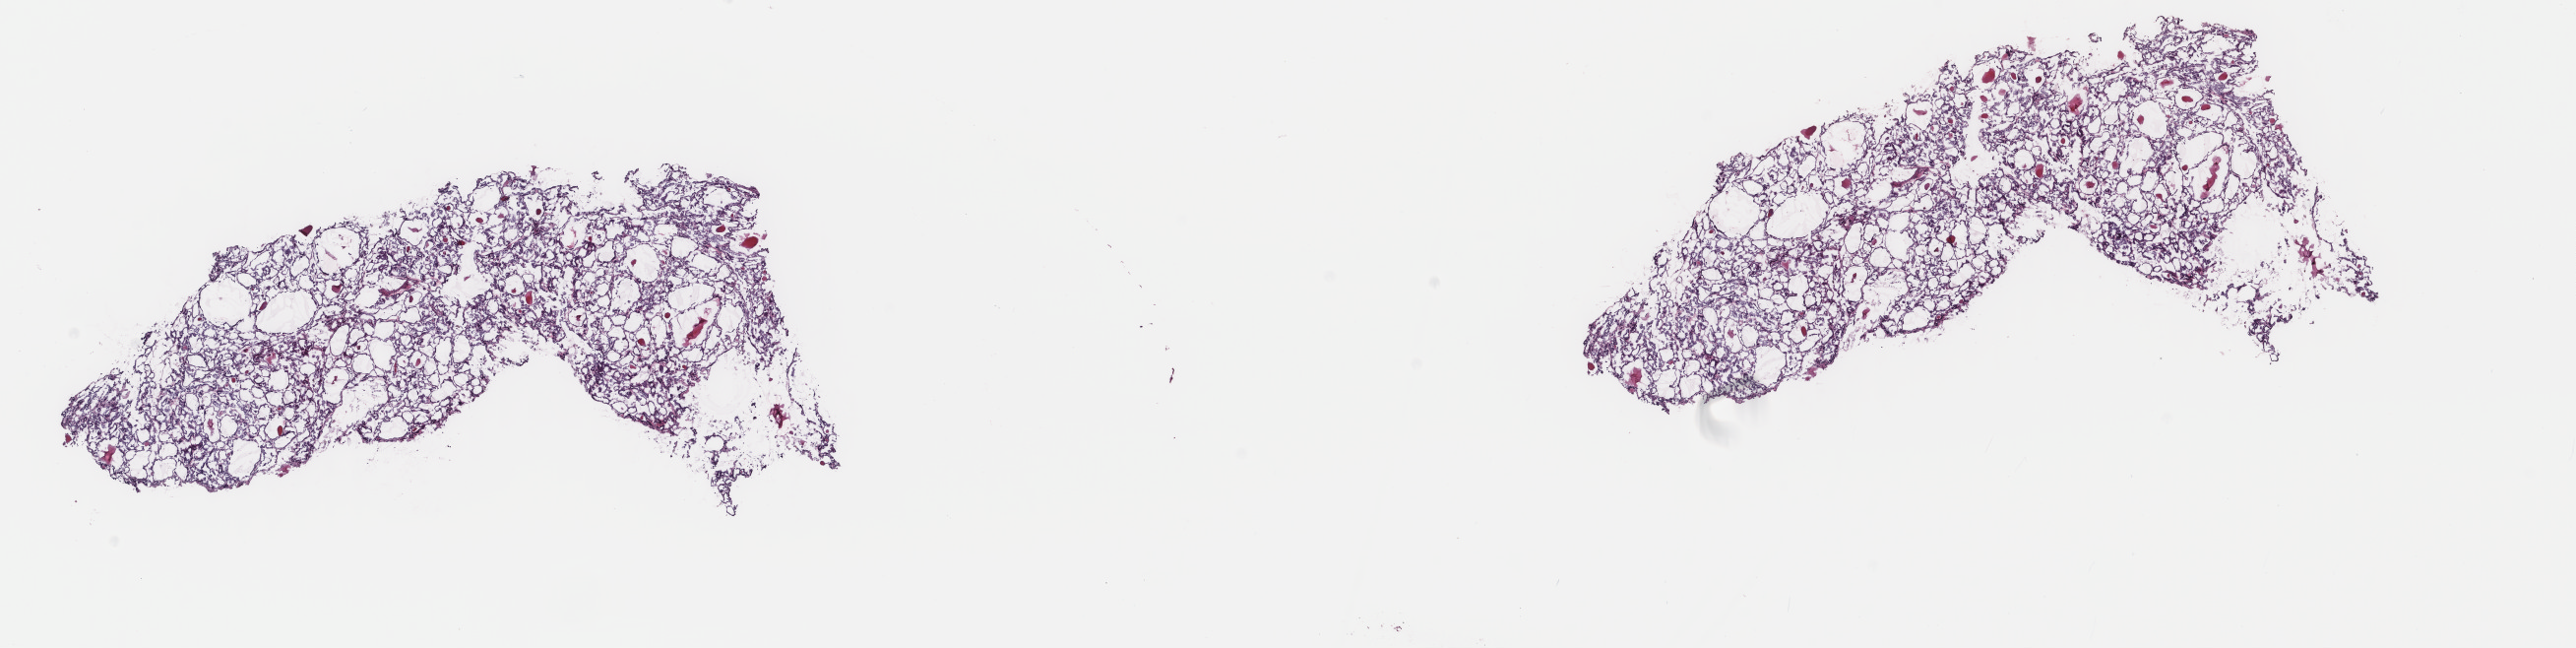
Whole-slide histology image, H&E — whole scanned area (about 20.8 x 5.2 mm, from a 40x scan) shown as a low-resolution overview; frozen section from the top of the tissue portion; sample: primary tumour, thyroid. Female, age 37 years at initial diagnosis. Composition of this section per pathologist review: tumour cells 90%, tumour nuclei 90%, normal cells 0%, stromal cells 10%, necrosis 0%. Infiltration values recorded for this section: lymphocyte infiltration 0%, monocyte infiltration 0%, neutrophil infiltration 0%.
Pathologic diagnosis: Papillary adenocarcinoma, NOS (thyroid gland). AJCC pathologic stage: I. Lymph nodes positive (case pathology): 1 of 7 examined. Laterality: left.